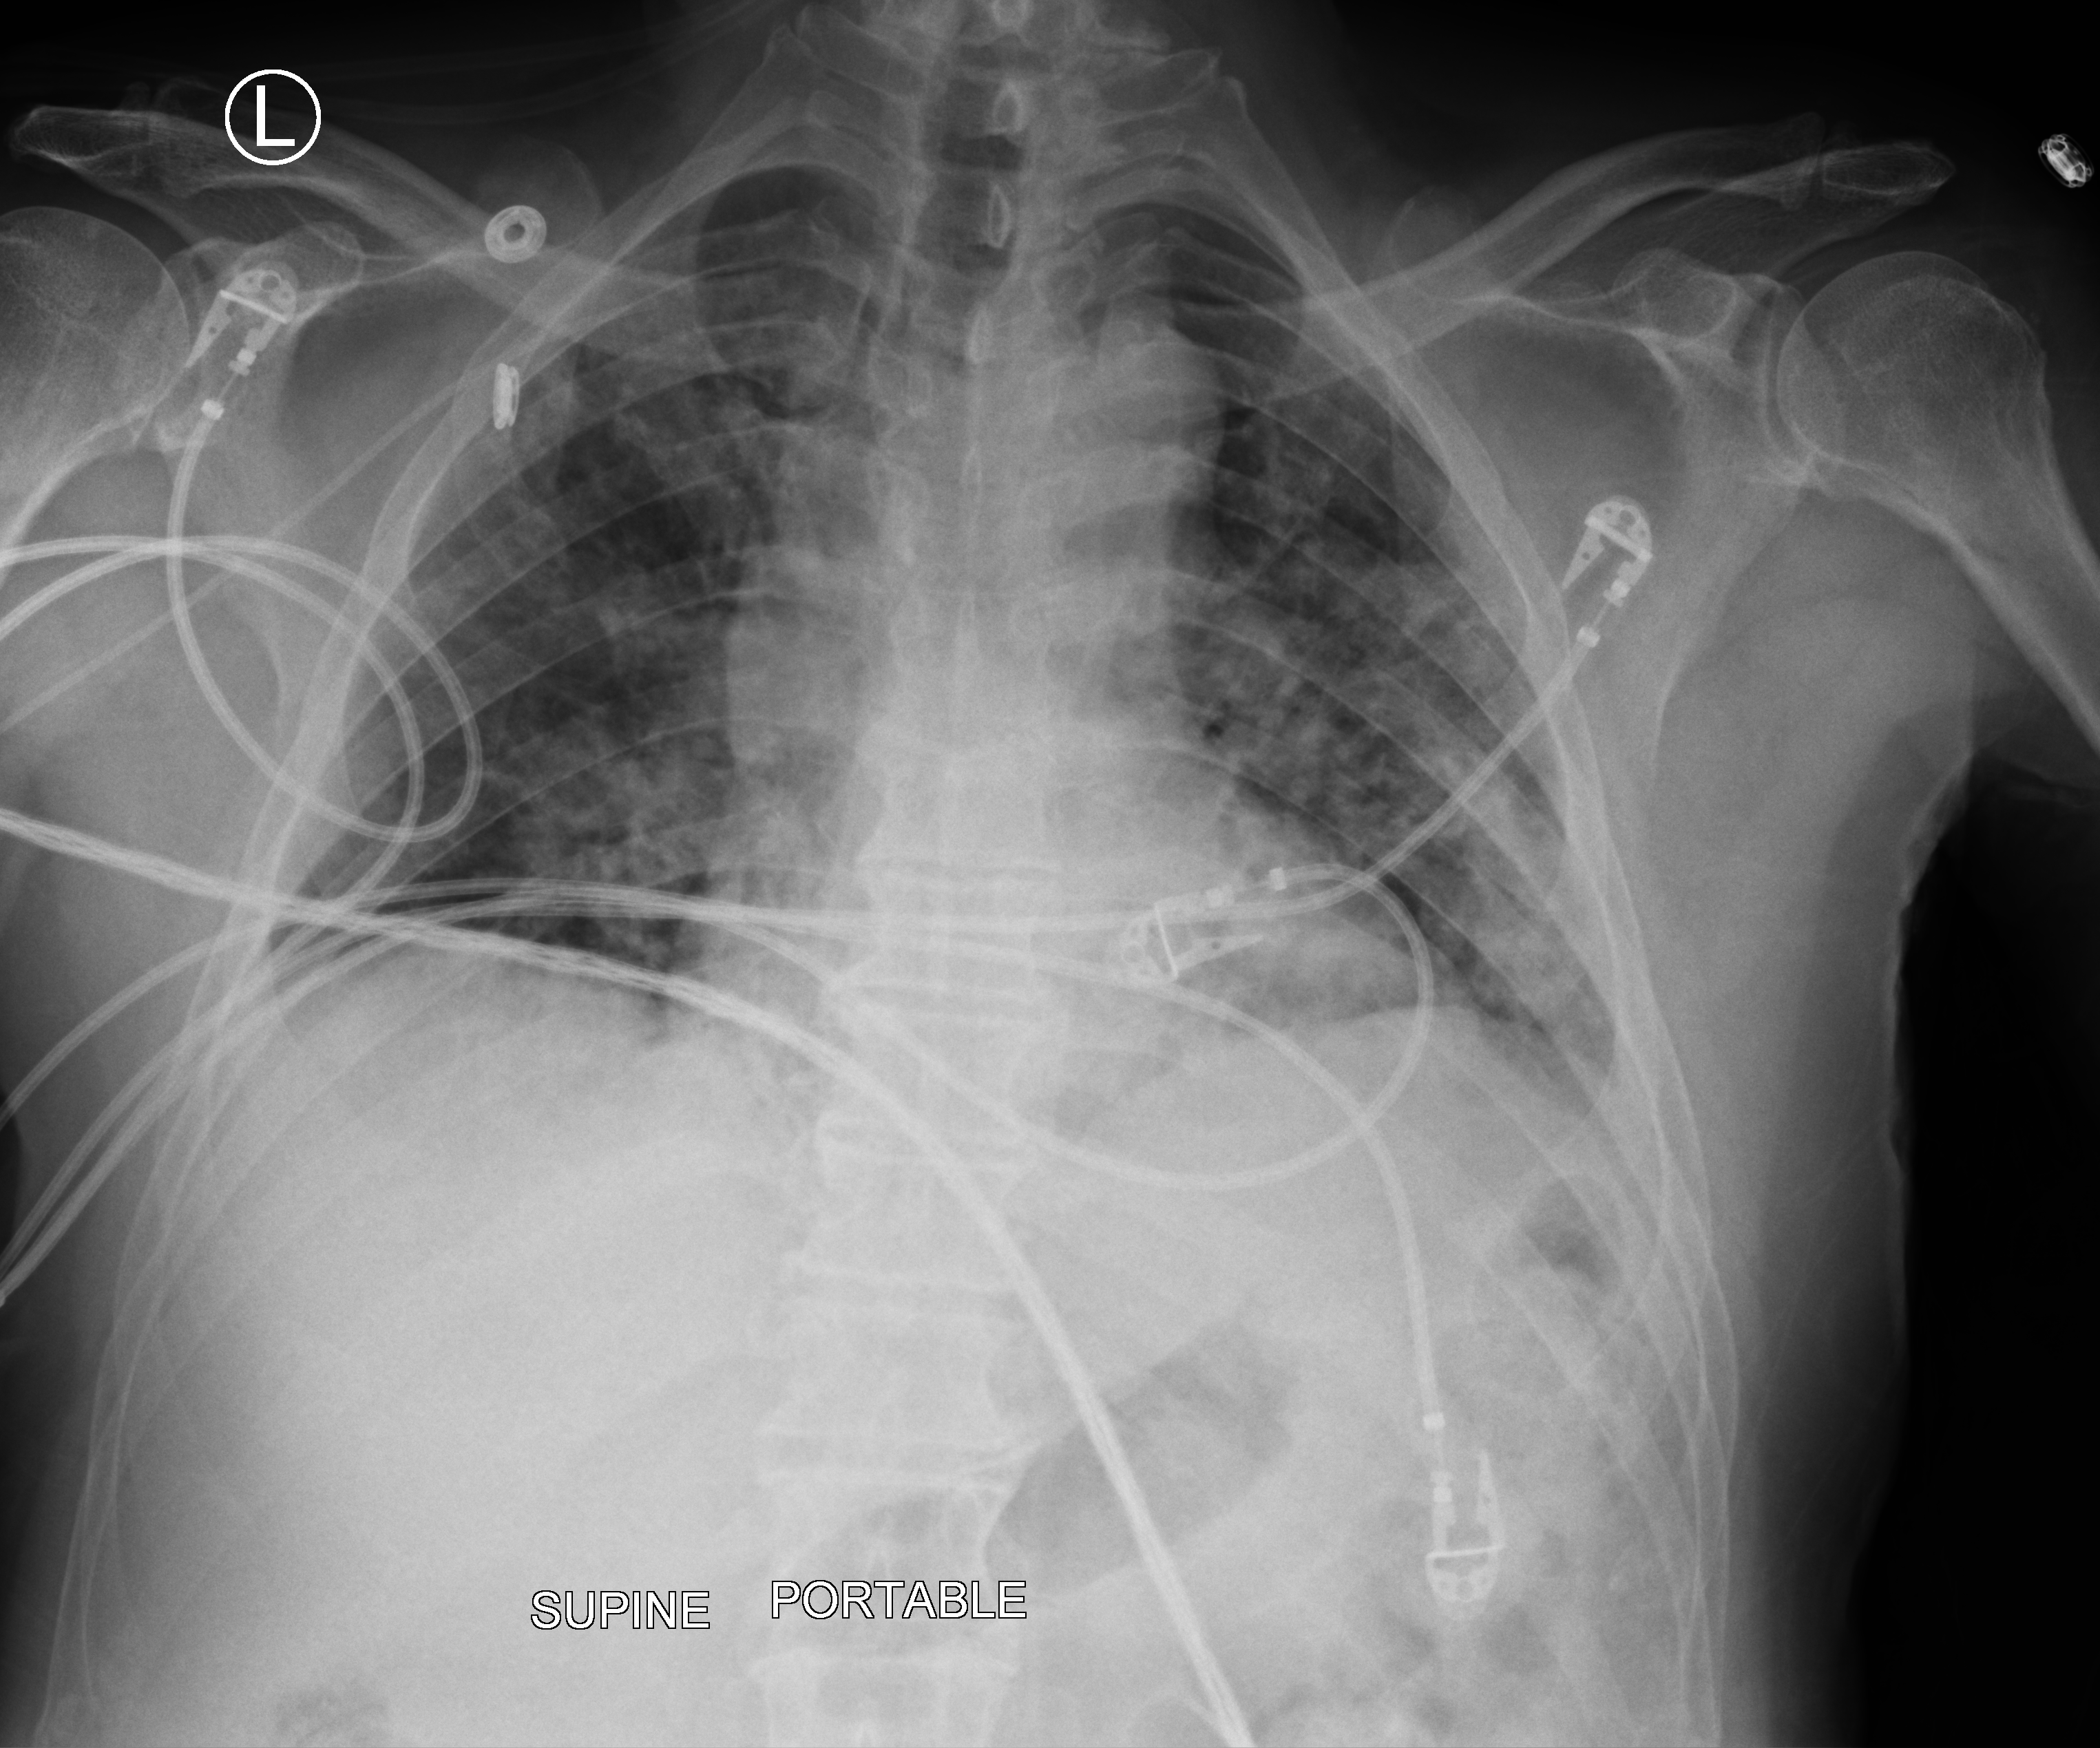
Portable chest radiograph; anteroposterior (AP) projection. Patient hospitalised with COVID-19; male, aged 60–74 years.
From the hospital-stay record, not from the radiograph (when in the stay this image was taken is not recorded):
- length of hospital stay: 20 days
- other chronic lung disease (admission record): no